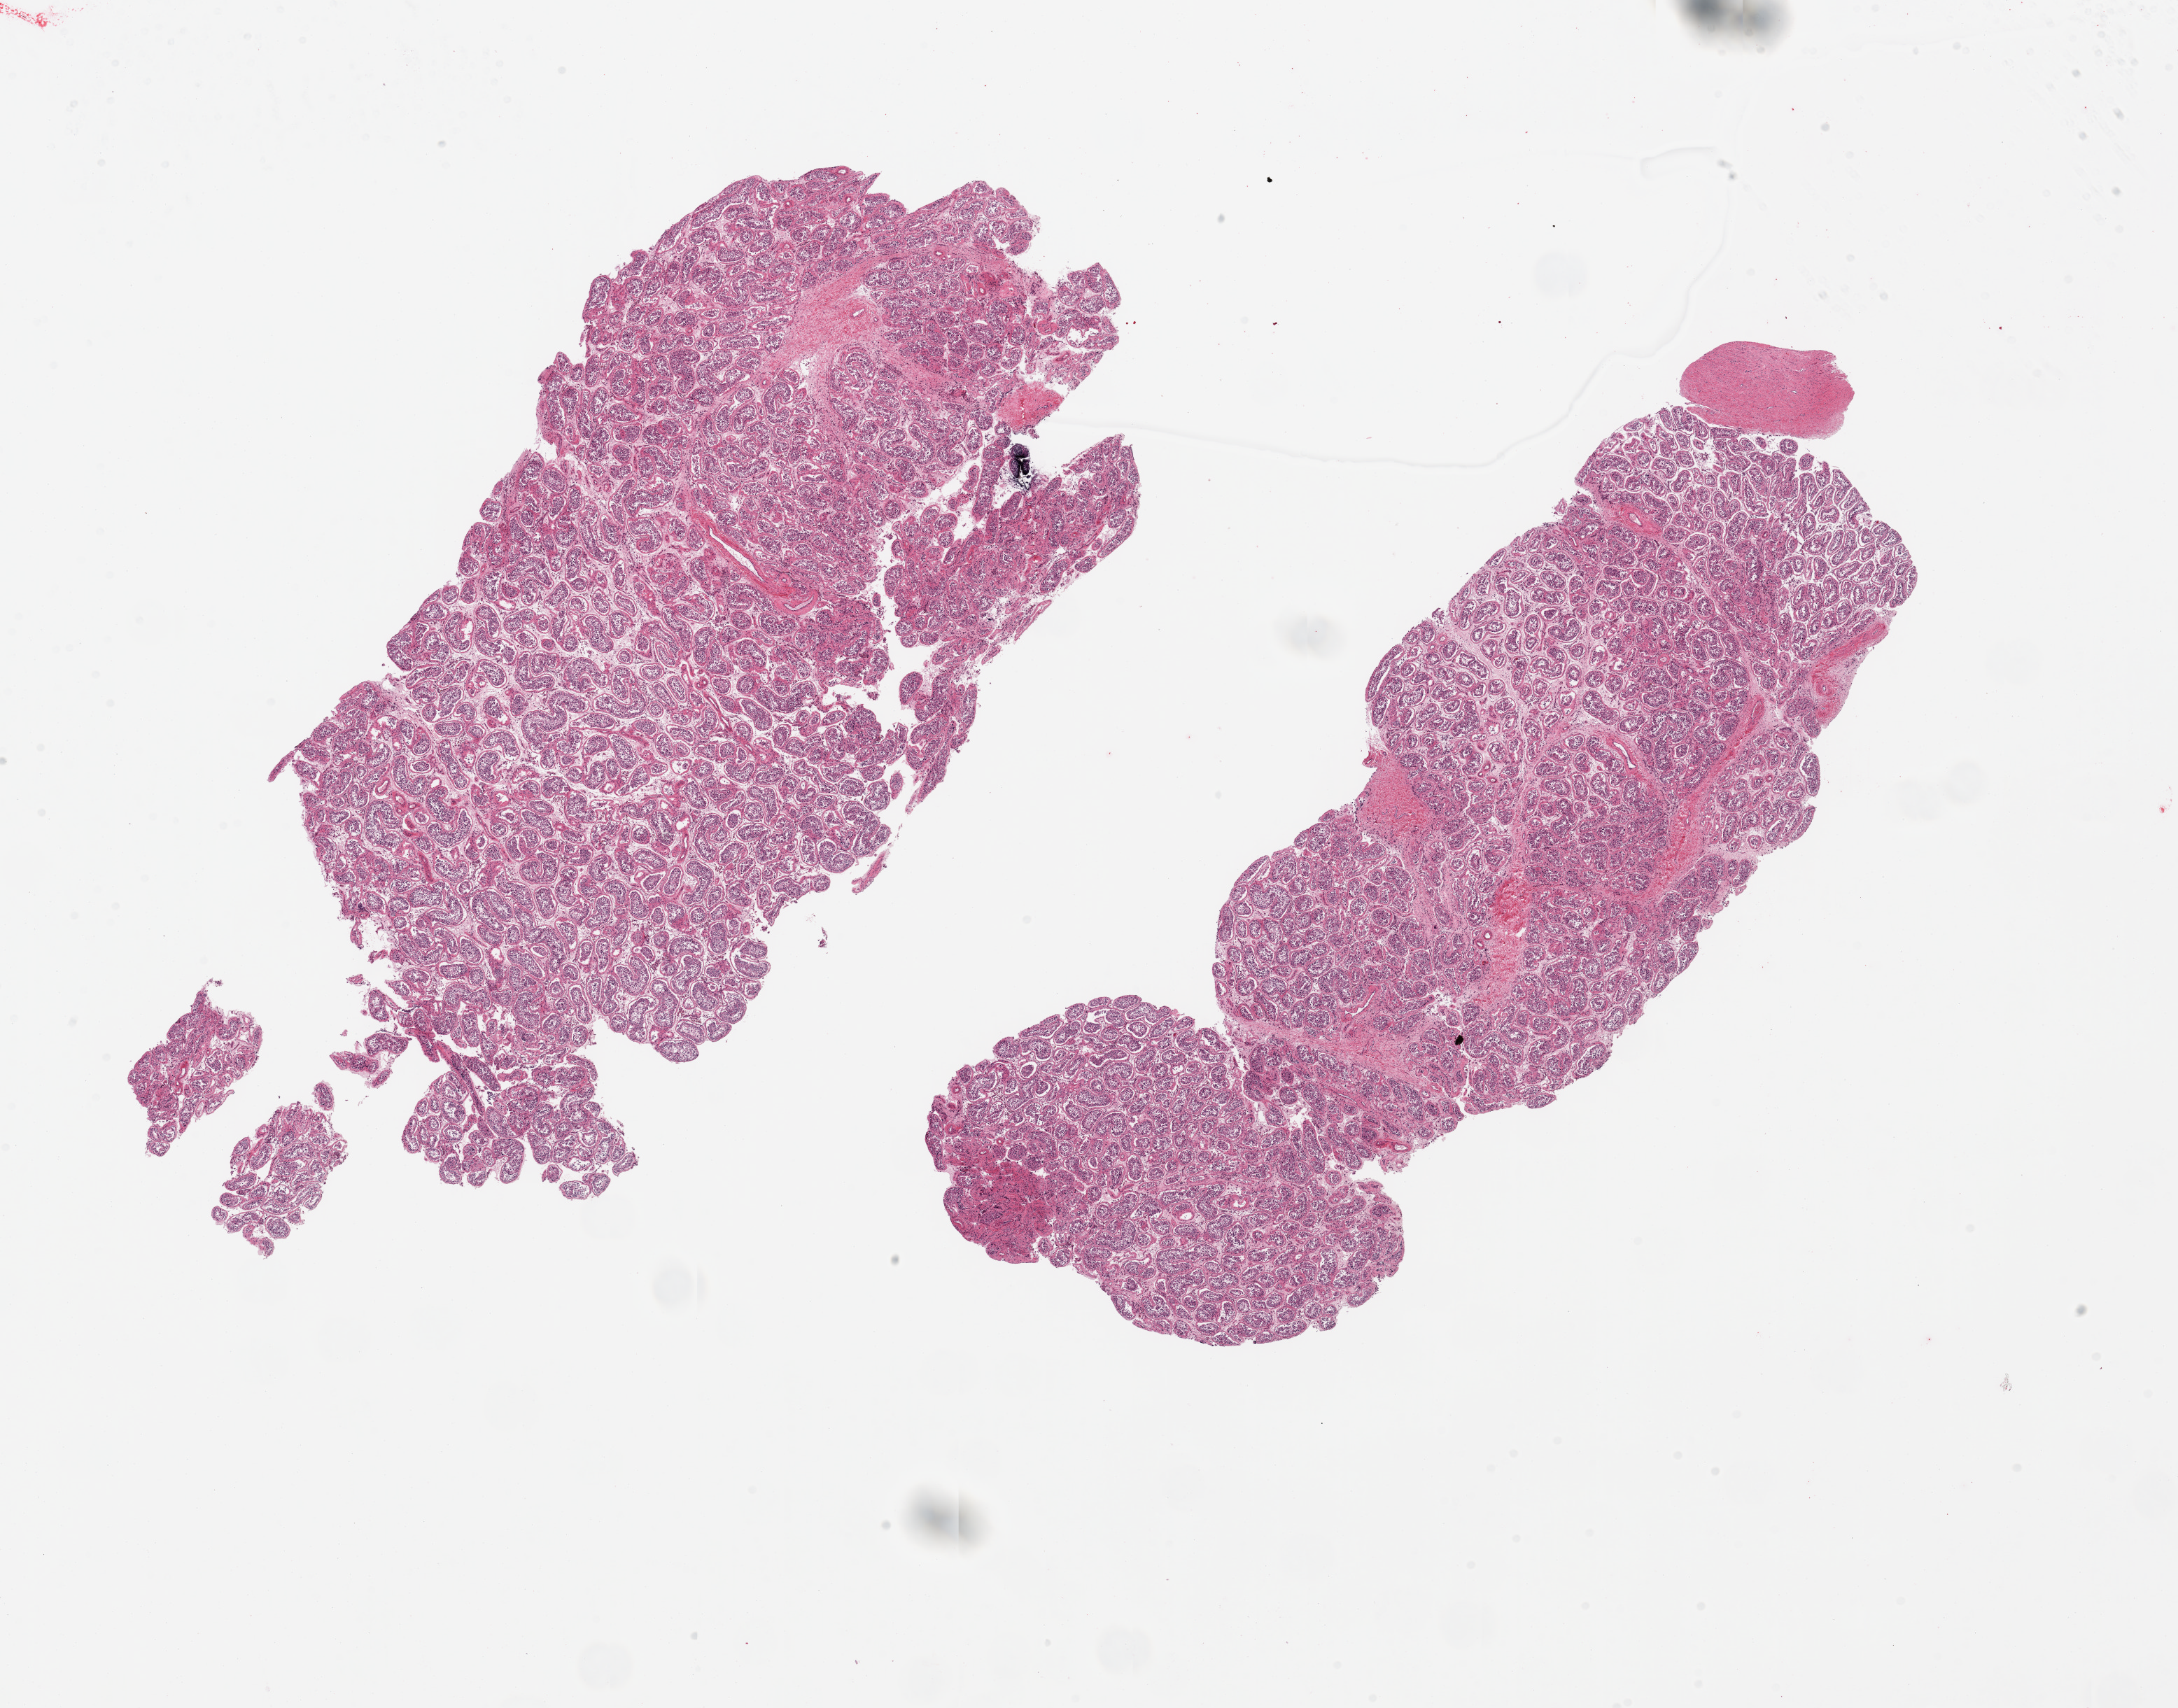
Whole-slide image, hematoxylin and eosin (H&E) stain, low-resolution overview of the scanned area, about 24.6 x 19.3 mm; PAXgene-fixed, paraffin-embedded tissue; target tissue: testis; tissue donor sample. Donor sex: male.
Reviewer comment on this tissue sample: 2 pieces; slightly reduced spermatogenesis.